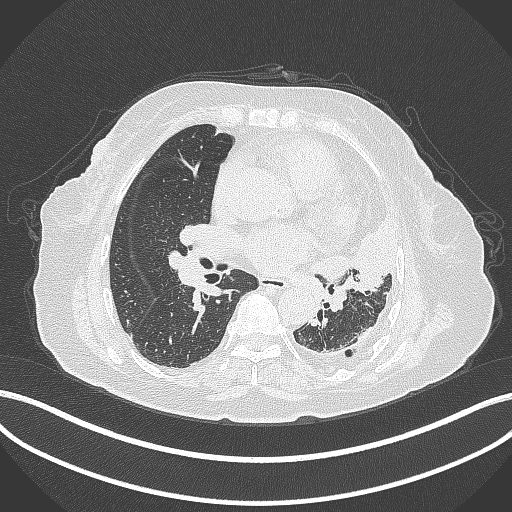
Chest CT, one axial slice. Position 184 of 399 along the scan axis. 120 kVp. Lung window (W 1500 / L -600 HU). 1 mm slice thickness. 512 × 512 image matrix, field of view 400 × 400 mm. Patient: female, 75 years. Case-level facts recorded for this patient, not image findings: clinical TNM (as recorded): T3 N3 M1.
Outlined on this slice (bounding box drawn by a radiologist):
- lung tumour (recorded histology: adenocarcinoma): box from (x=305, y=208) to (x=402, y=296) px